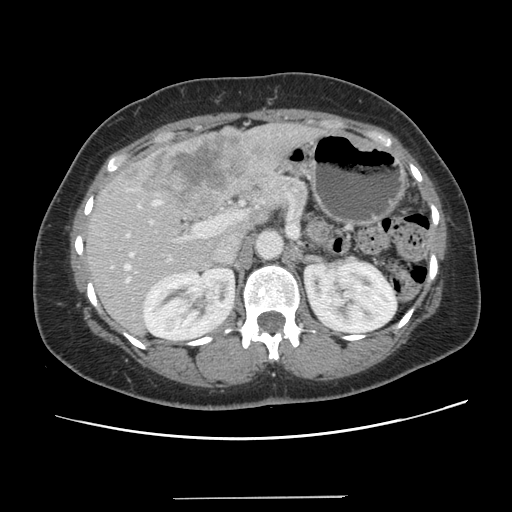
Contrast-enhanced abdominal CT, one axial slice; slice 72 of 141 in the series (ordered by position); 120 kVp; intravenous contrast given; soft-tissue window (W 400 / L 40 HU); 2.5 mm slice thickness; 512 × 512 image matrix, field of view 366 × 366 mm. Female patient, age 53 years. Case-level facts recorded for this patient, not image findings: diagnosis: colorectal cancer liver metastases, imaged before liver resection; multiple liver metastases: no; largest metastasis: 14.5 cm; disease in both lobes: yes.
Structures marked on this image (expert manual segmentation):
- hepatic veins: bounding box (x1, y1, x2, y2) in pixels: (124, 252, 132, 281)
- liver: (87, 123, 317, 333)
- planned liver remnant (the part of the liver to remain after resection): (88, 207, 251, 333)
- portal vein (with intrahepatic branches): (126, 200, 245, 237)
- liver metastasis: (127, 132, 260, 204)